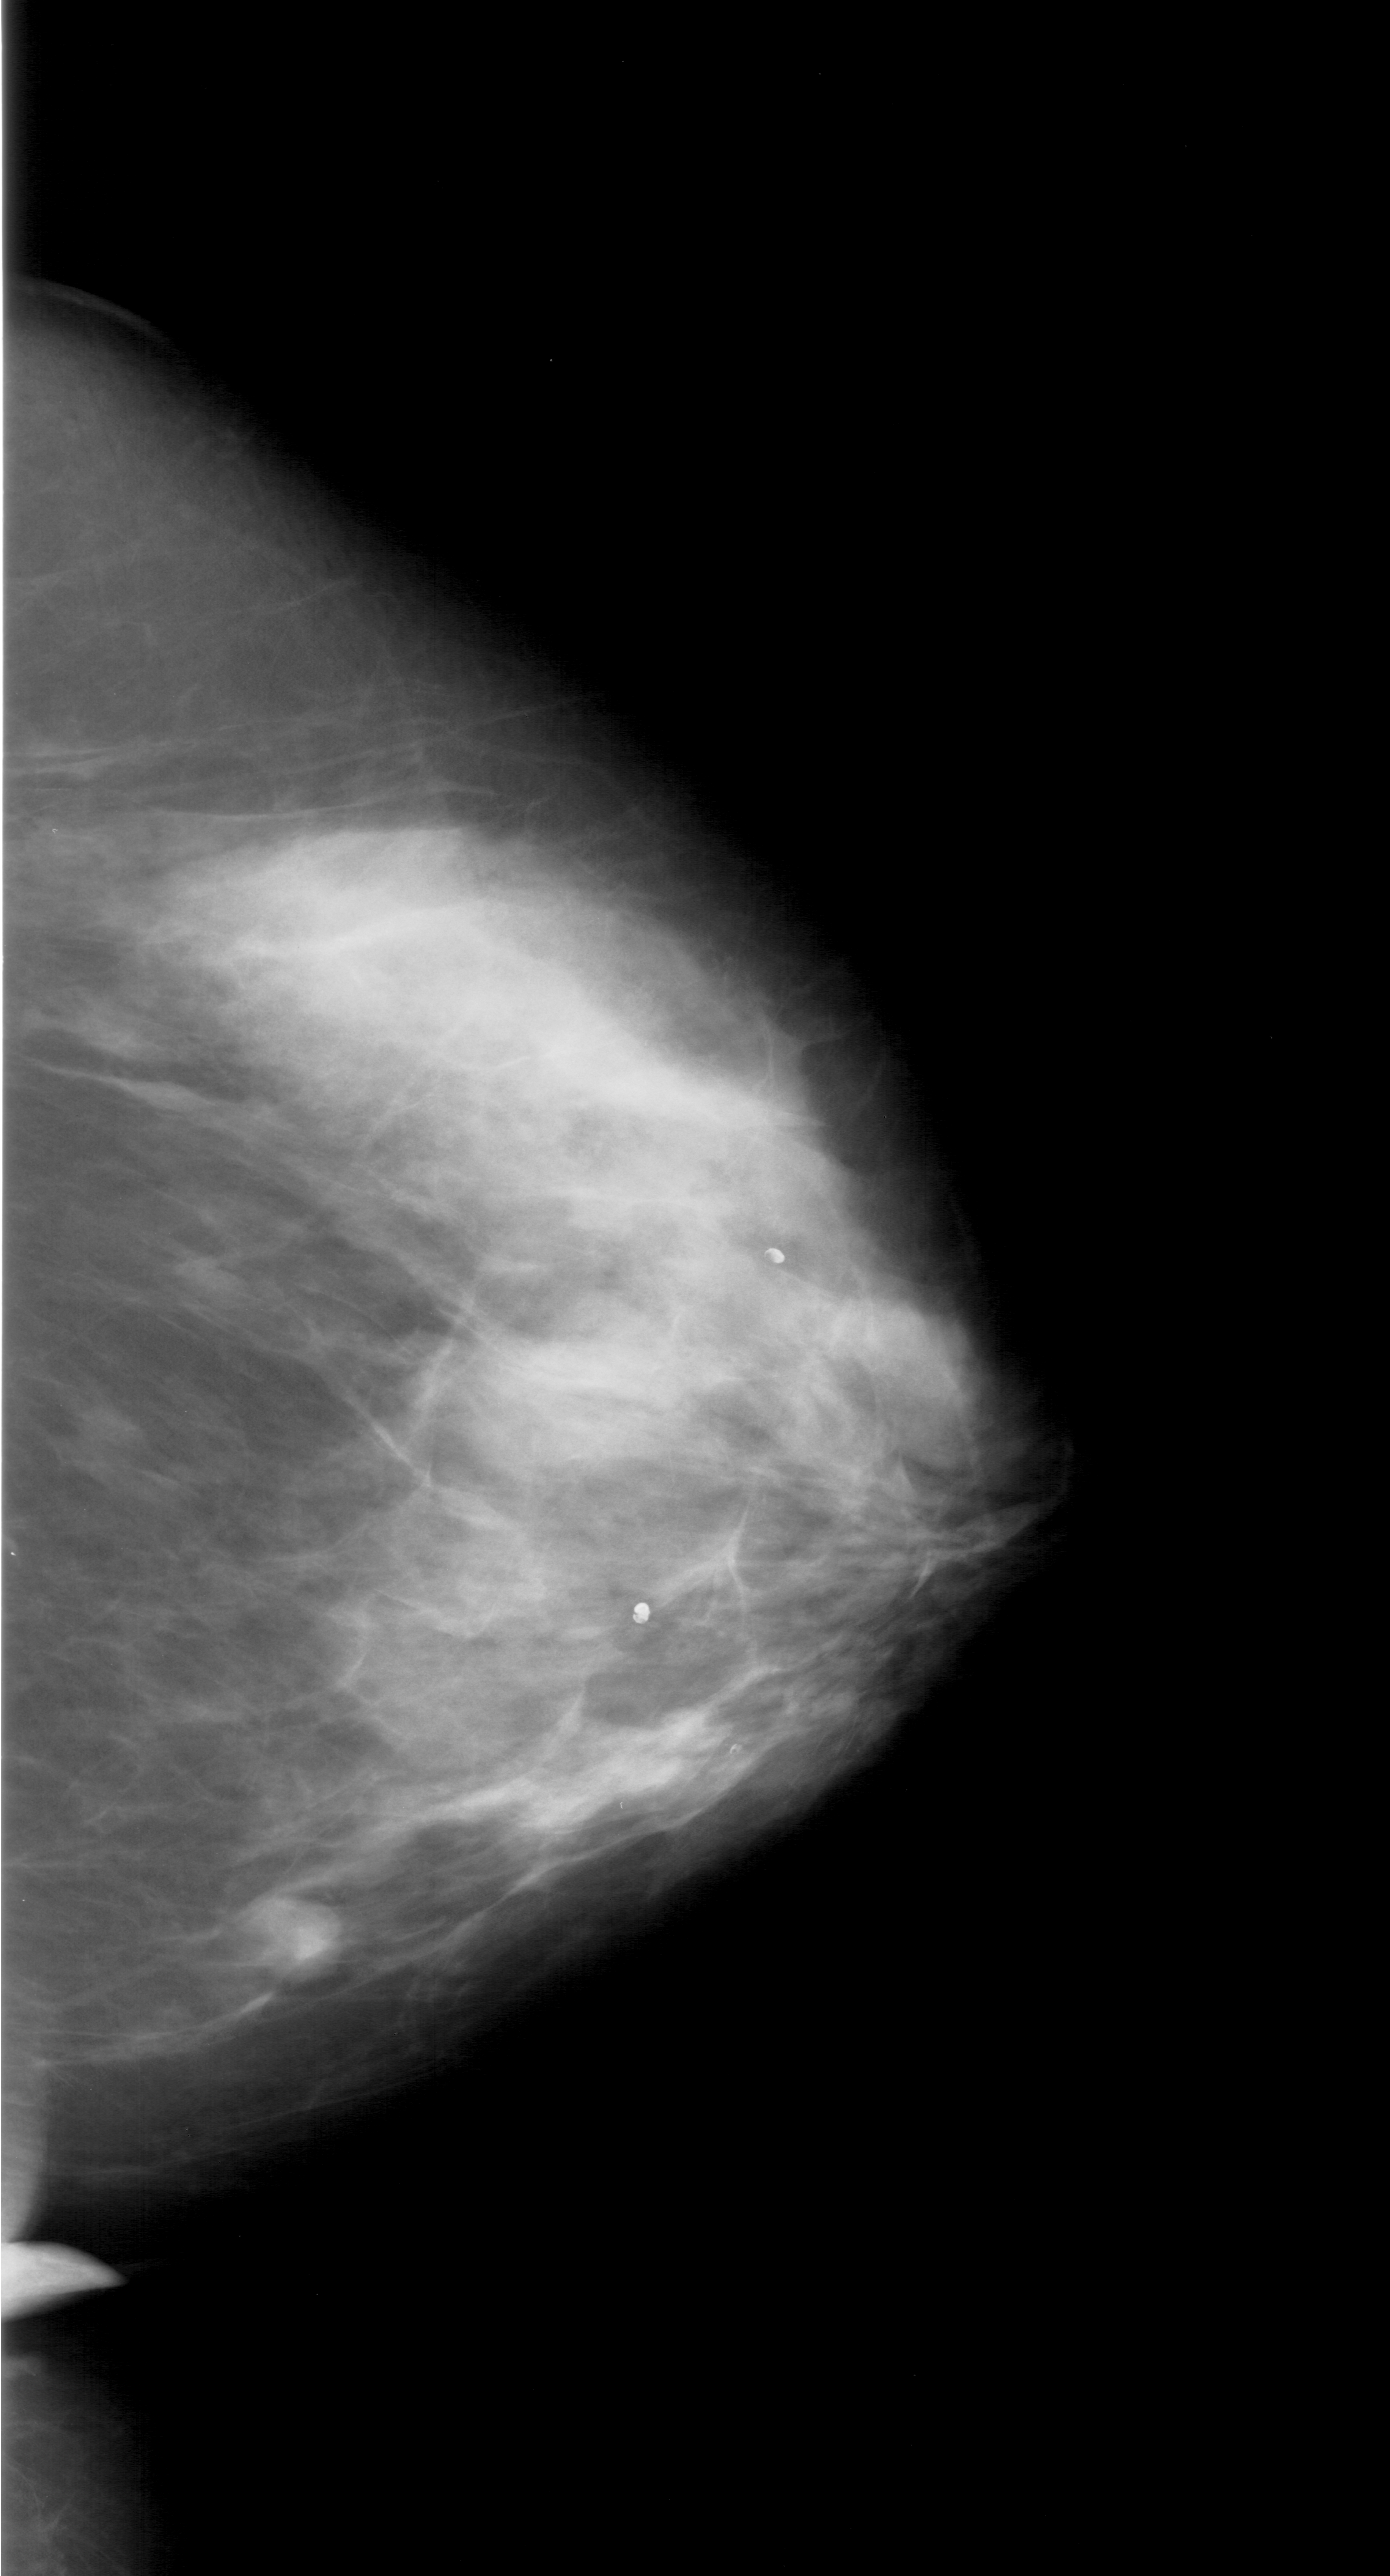
Scanned film-screen mammogram; right breast; craniocaudal (CC) view; BI-RADS breast density category 4 (scale 1–4); 1390 × 2576 image matrix.
Marked abnormalities (boxes around the expert regions of interest):
- mass, shape lobulated, margins ill defined; BI-RADS assessment category 4; pathology (as recorded): malignant: bounding box [x1, y1, x2, y2] px = [245, 1891, 357, 1987]